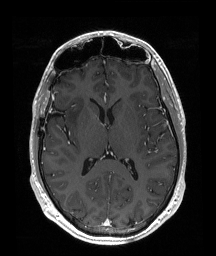
Brain MRI from a brain-tumour surgery series, one axial slice. Slice 99 of 192 in the series (ordered by position). T1-weighted post-contrast. 216 × 256 image matrix. From the clinical record (not read from this slice): histopathology: Astrocytoma; WHO grade: 2; IDH mutation: yes.
Outlined on this slice (outlined manually by an expert reader):
- tumour: bounding box (x1, y1, x2, y2) in pixels: (66, 96, 85, 127)